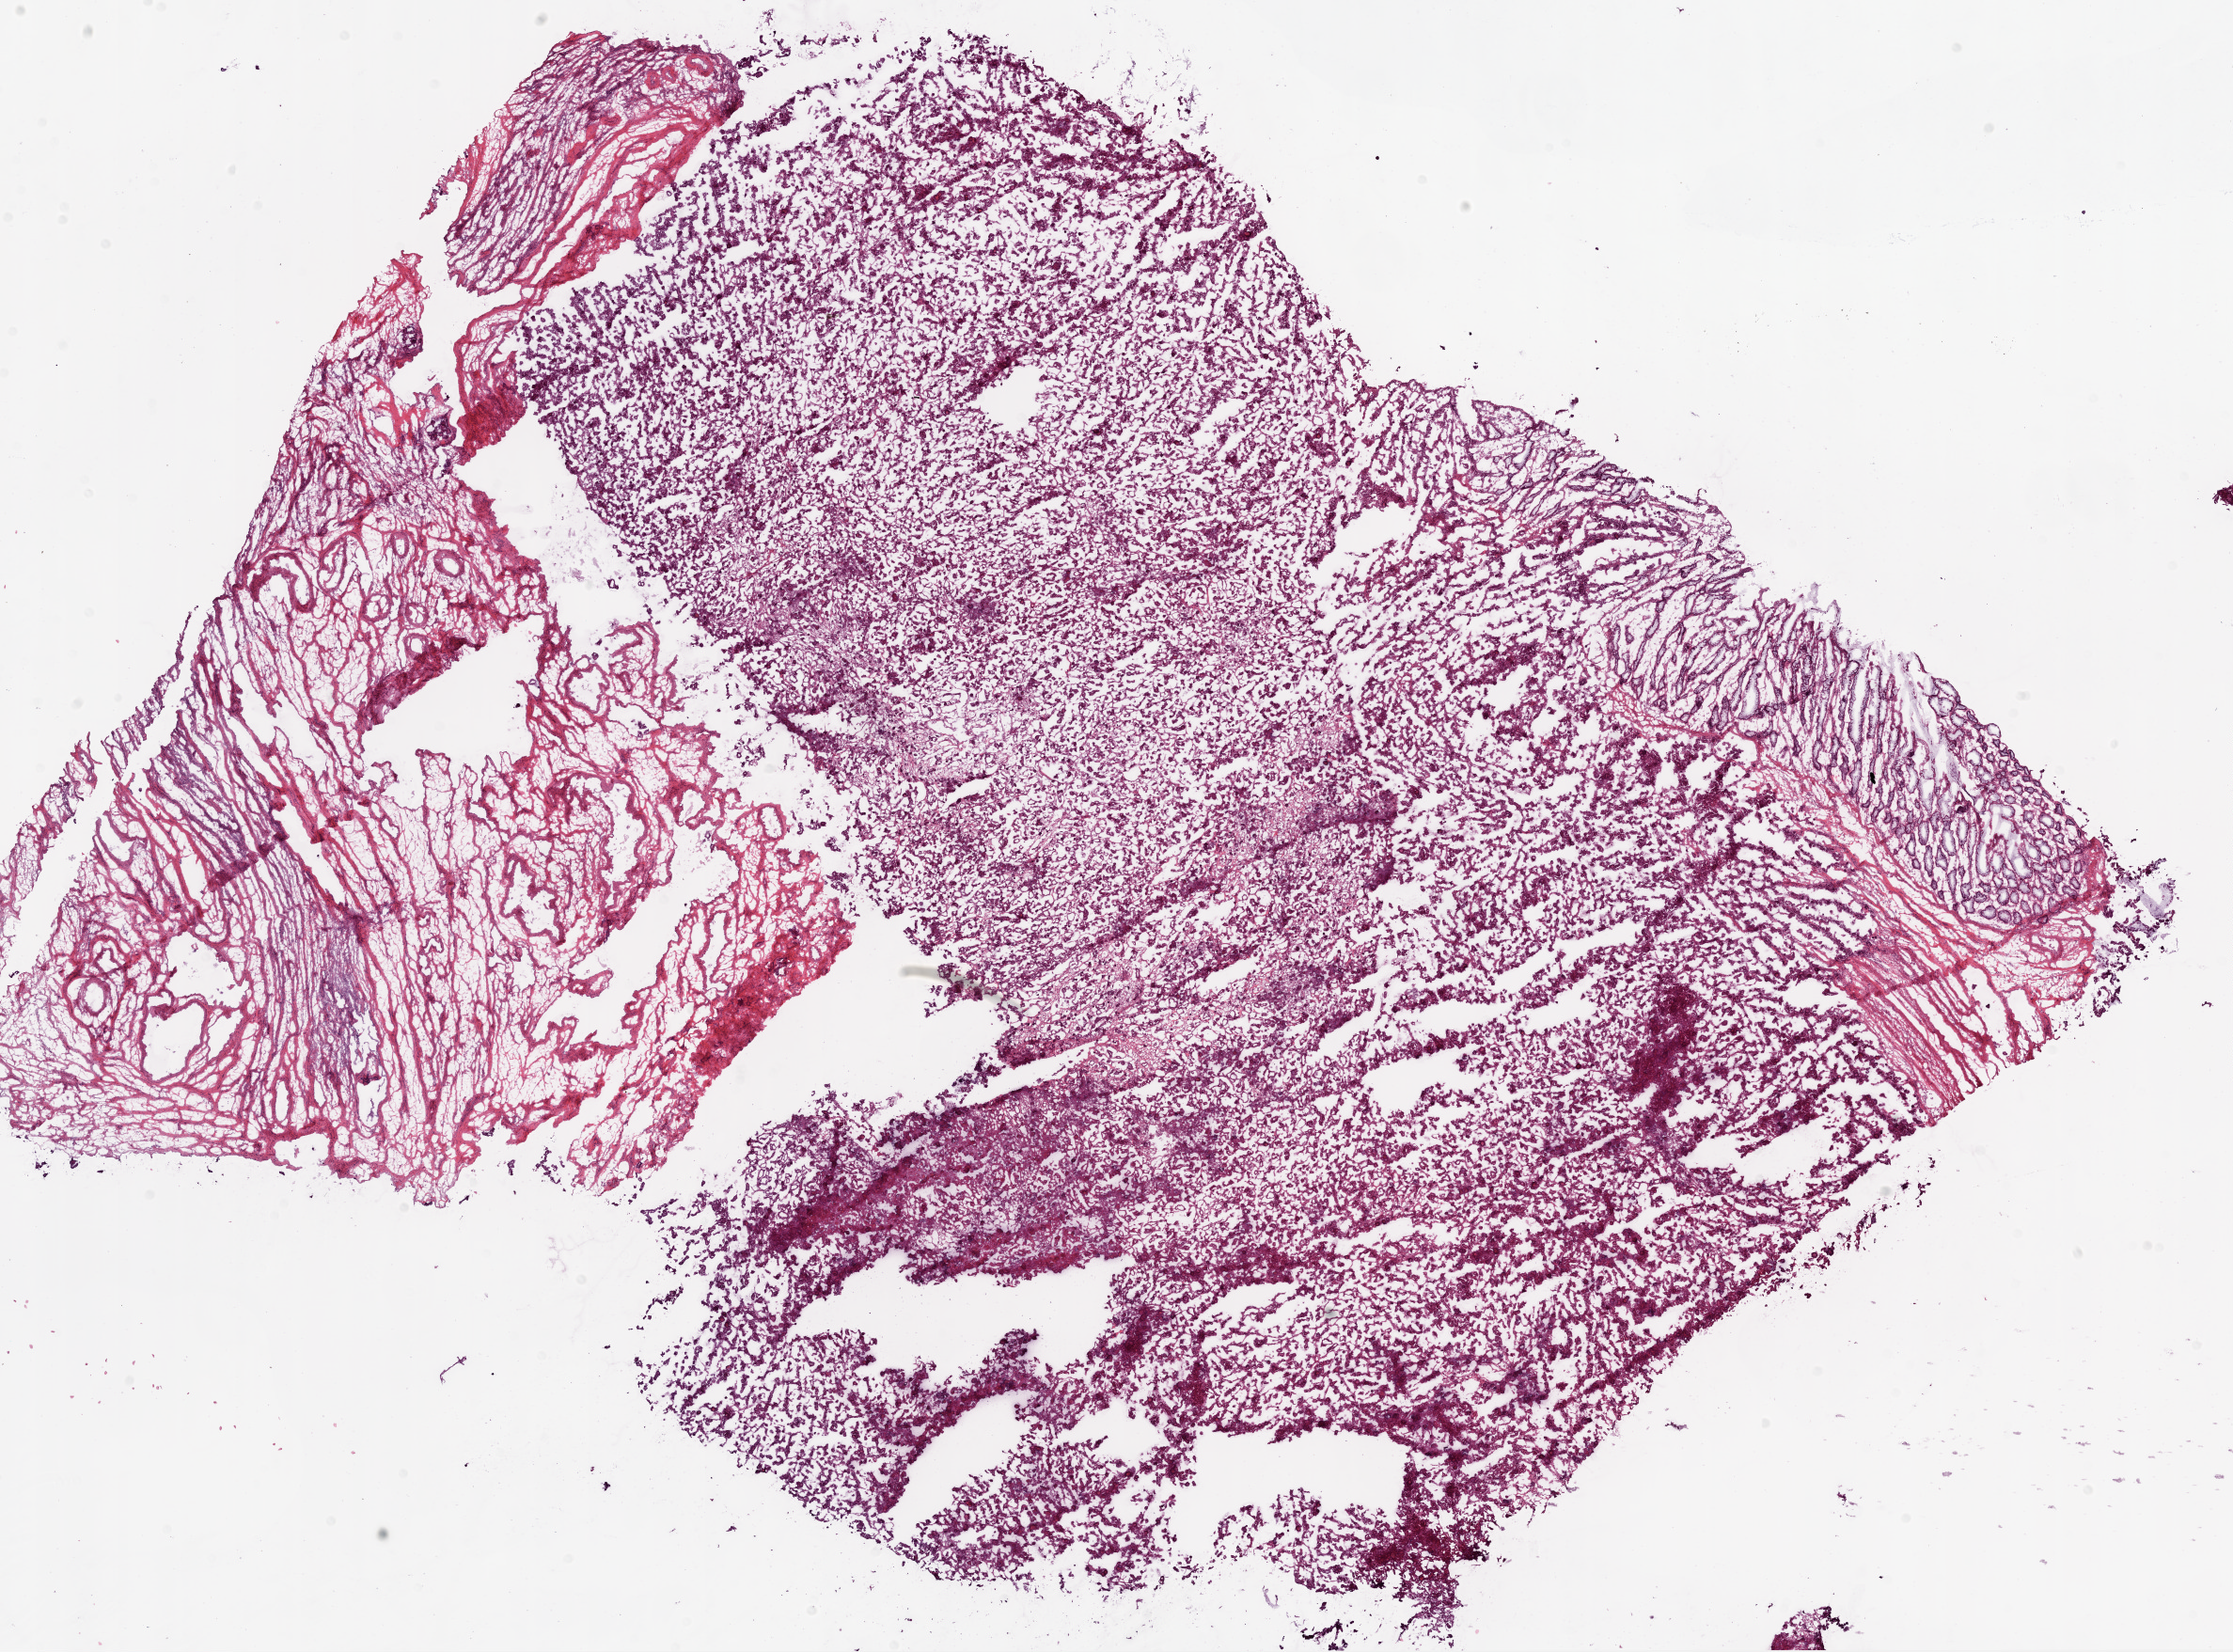
Whole-slide histology image, H&E-stained, whole scanned area (about 19.1 x 14.1 mm, acquisition: 20x scan) shown as a low-resolution overview. Frozen section from the bottom of the tissue portion. Sample: primary tumour, ovary. Female, age 48 years at initial diagnosis. Histologic grade: G2 (moderately differentiated). Pathologist review of this section (percent, as recorded): tumour cells 70%, tumour nuclei 80%, normal cells 0%, stromal cells 30%, necrosis 0%.
• diagnosis: Serous cystadenocarcinoma, NOS
• FIGO stage: IV